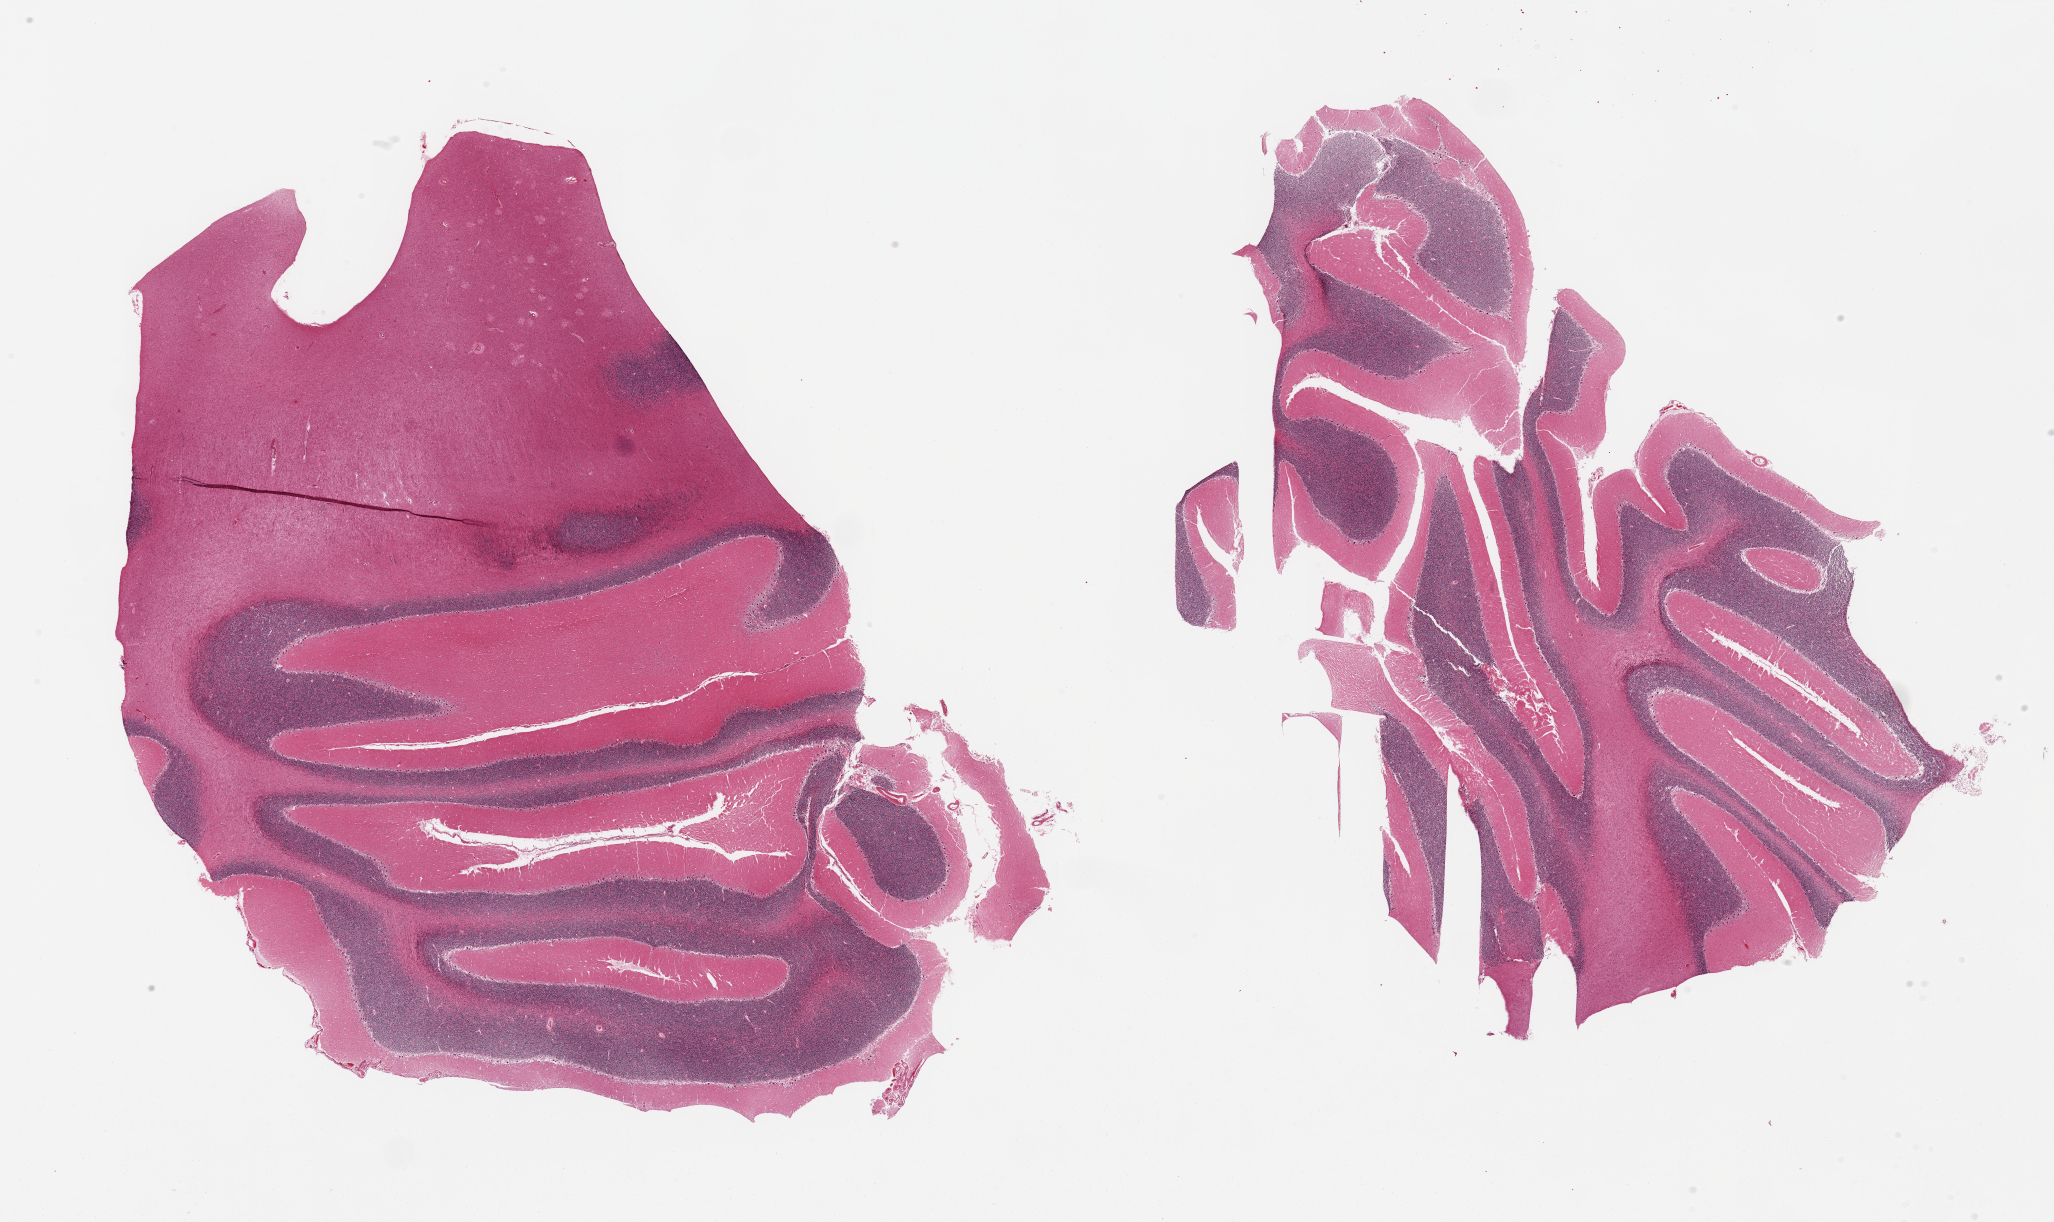
Hematoxylin and eosin (H&E) whole-slide image — low-resolution overview of the scanned area, about 32.5 x 19.3 mm (from a 20x scan); PAXgene-fixed paraffin-embedded (PFPE) section; target tissue: cerebellum; donor tissue sample. Donor sex: male.
Pathologist's review note for this sample: 2 pieces; oversized, Purkinje cells well visualized.